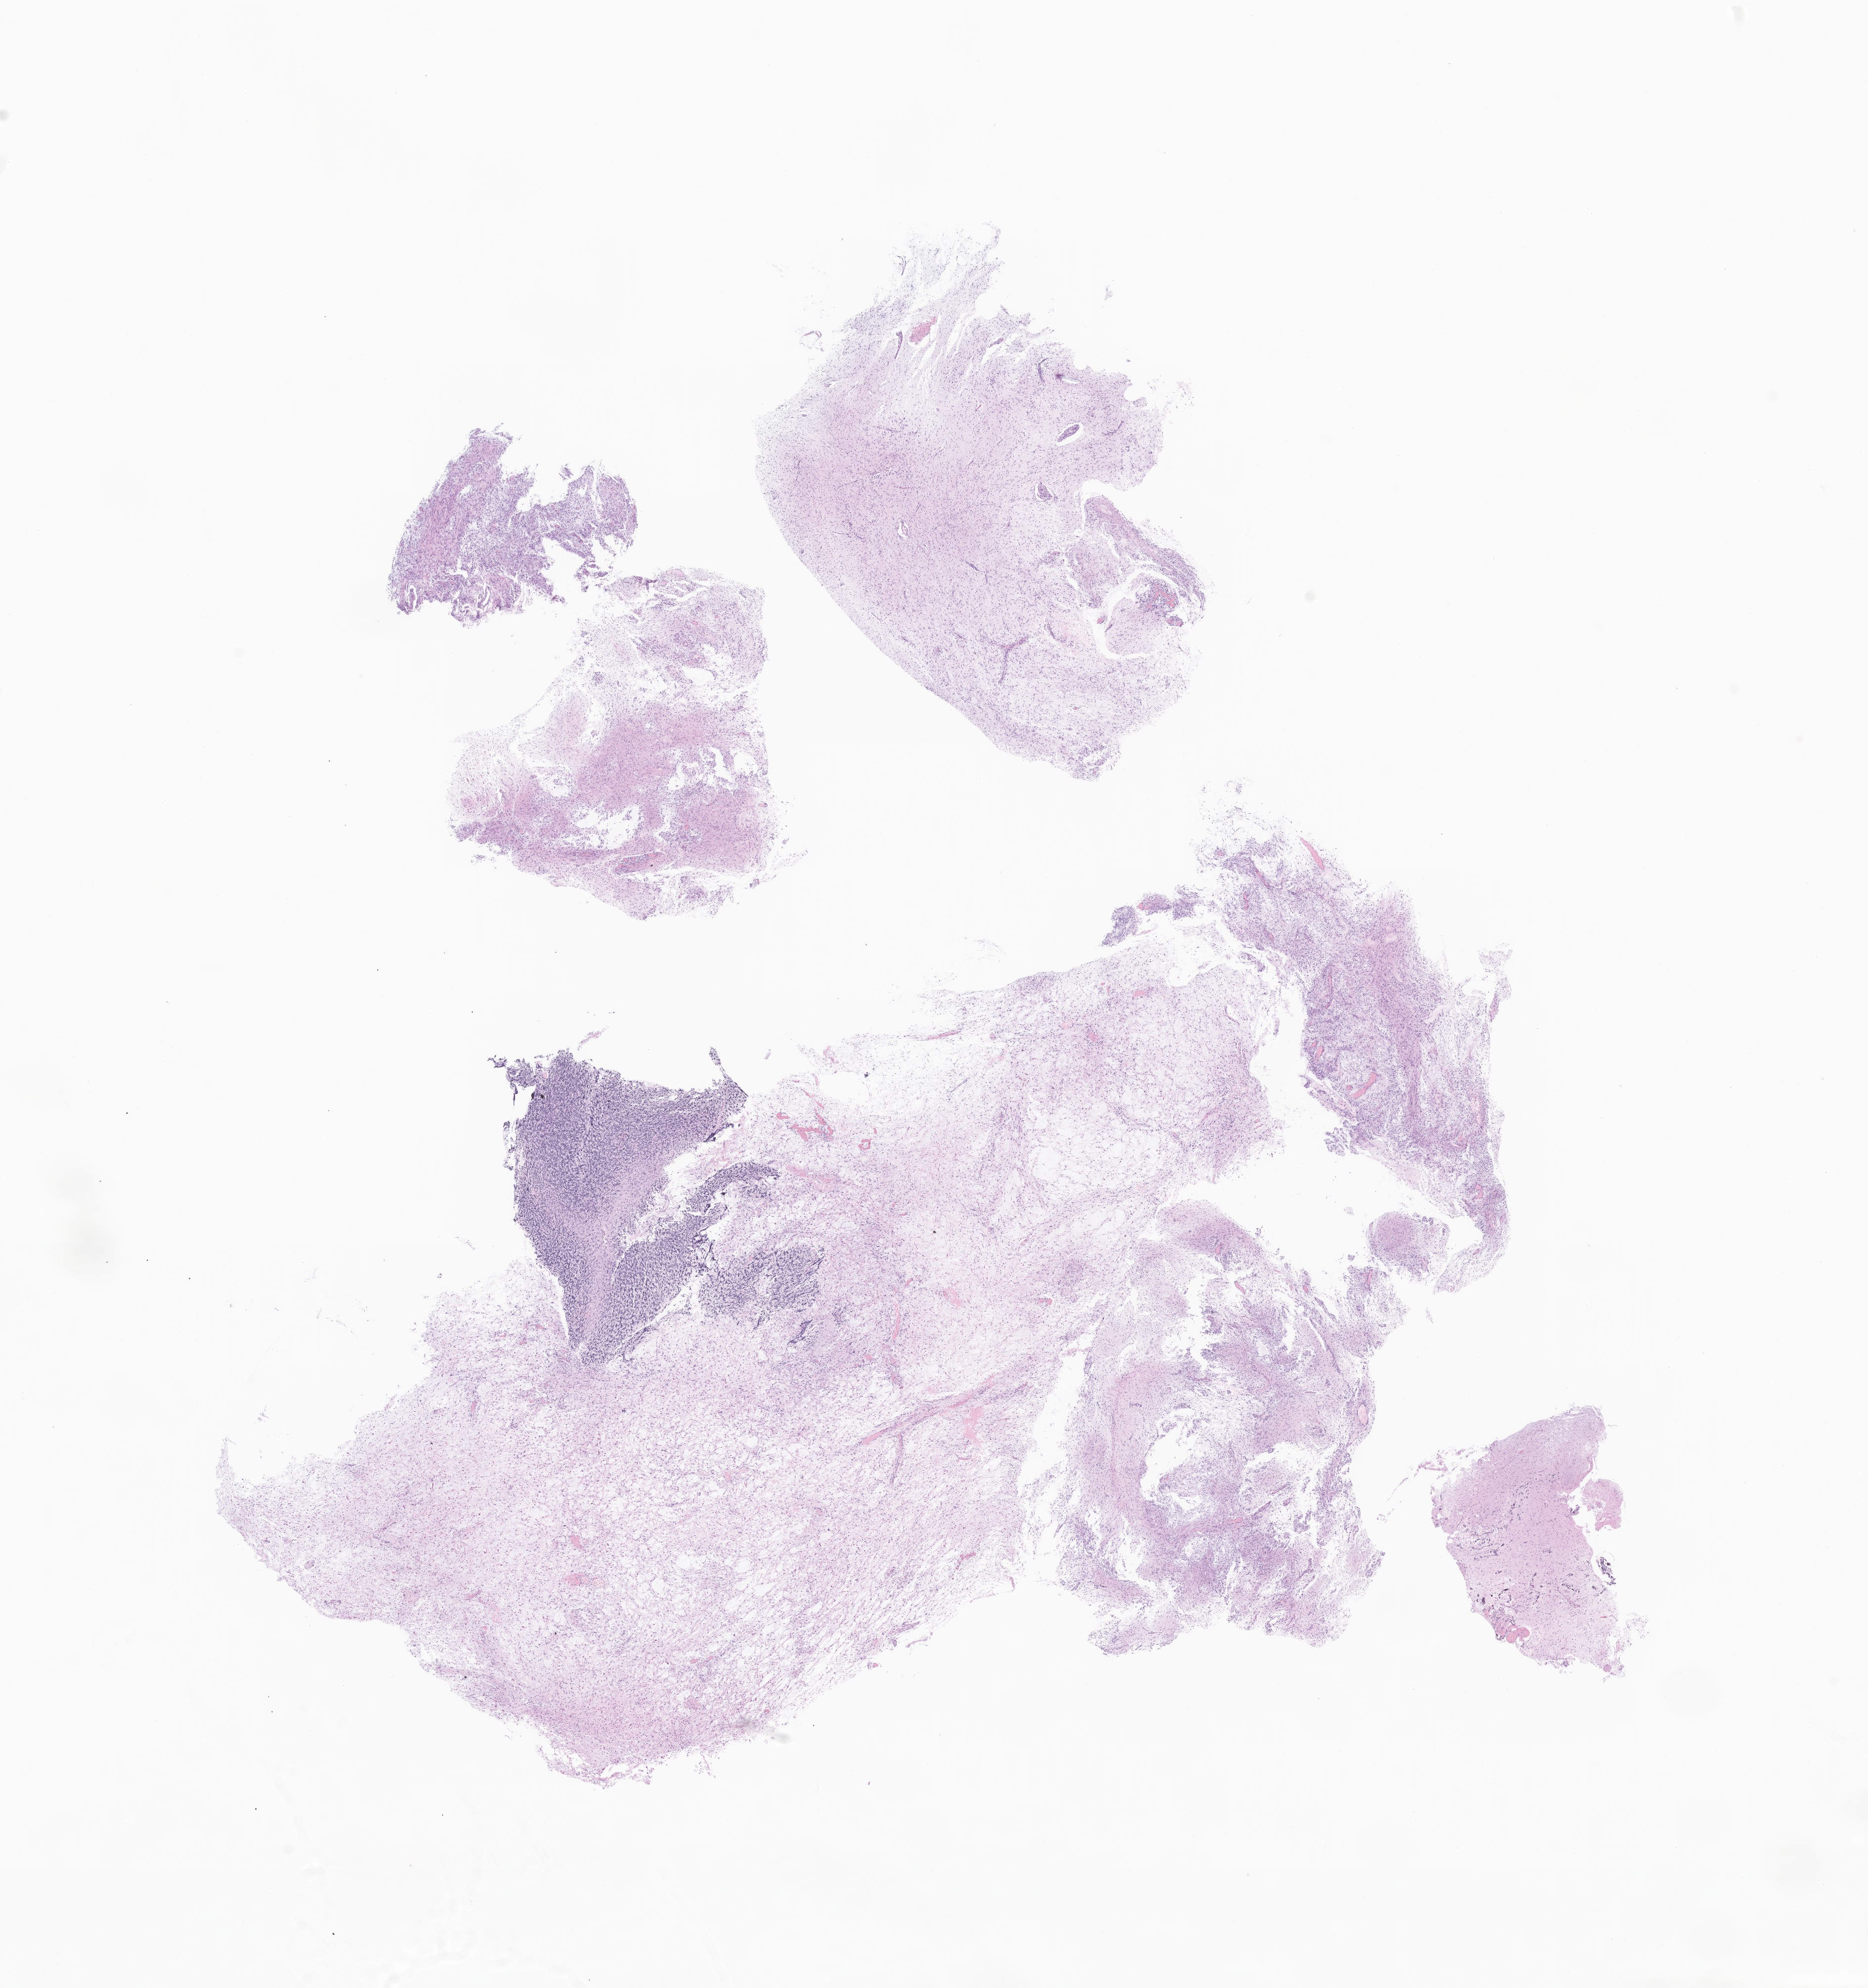
Hematoxylin and eosin (H&E) whole-slide image of tumor tissue from the brain, whole scanned area (about 15.9 x 16.9 mm) shown as a low-resolution overview, formalin-fixed paraffin-embedded section. Patient: male, age 200 months (16 years 8 months).
Diagnosis: Pilocytic astrocytoma.